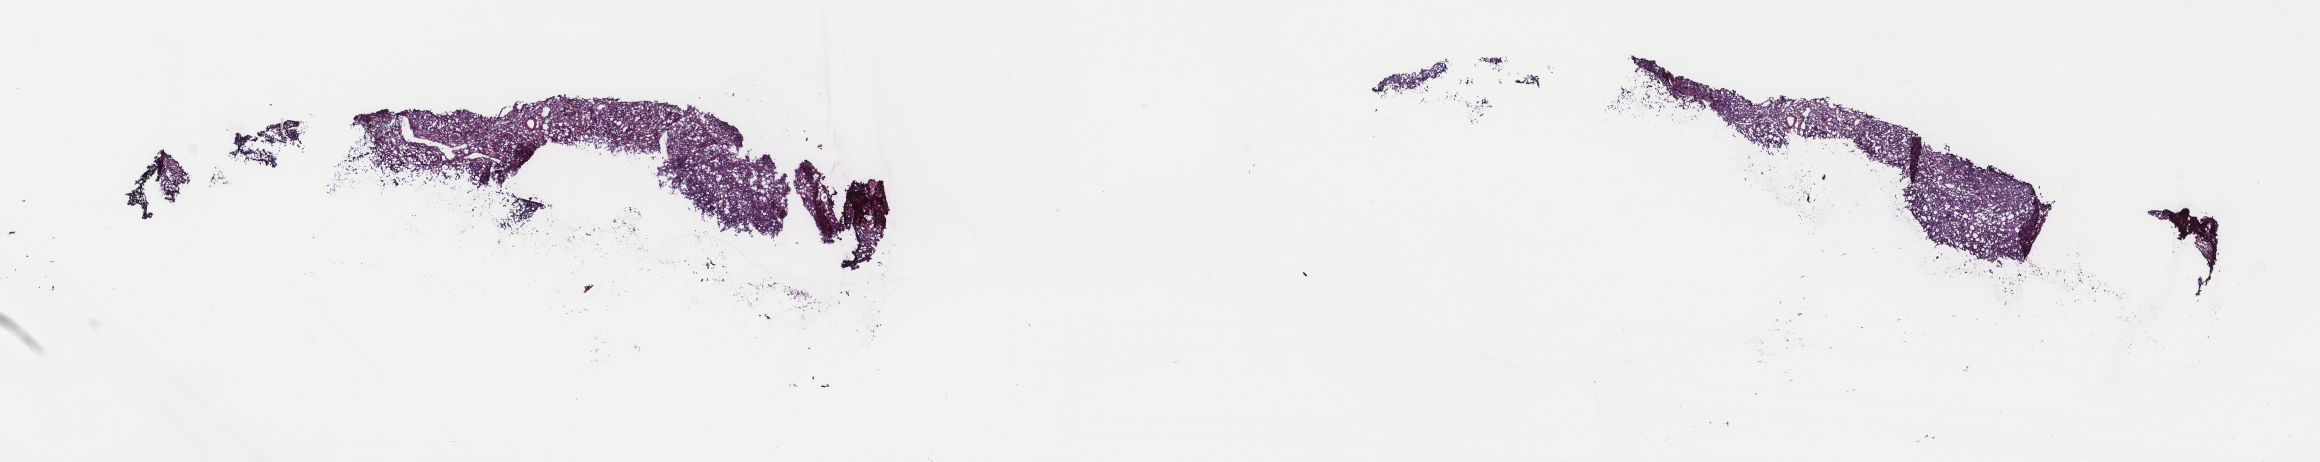
Hematoxylin and eosin (H&E) stained whole-slide image, low-resolution overview of the scanned area, about 18.4 x 3.7 mm; frozen section from the top of the tissue portion; cervix, primary tumour sample. Female, age 43 years at initial diagnosis. Histologic grade: G2 (moderately differentiated). Pathologist review of this section (percent, as recorded): tumour cells 65%, tumour nuclei 70%, normal cells 0%, stromal cells 30%, necrosis 5%. Infiltration values recorded for this section: lymphocyte infiltration 10%, monocyte infiltration 3%, neutrophil infiltration 0%.
- diagnosis: Squamous cell carcinoma, keratinizing, NOS
- FIGO stage: IB1